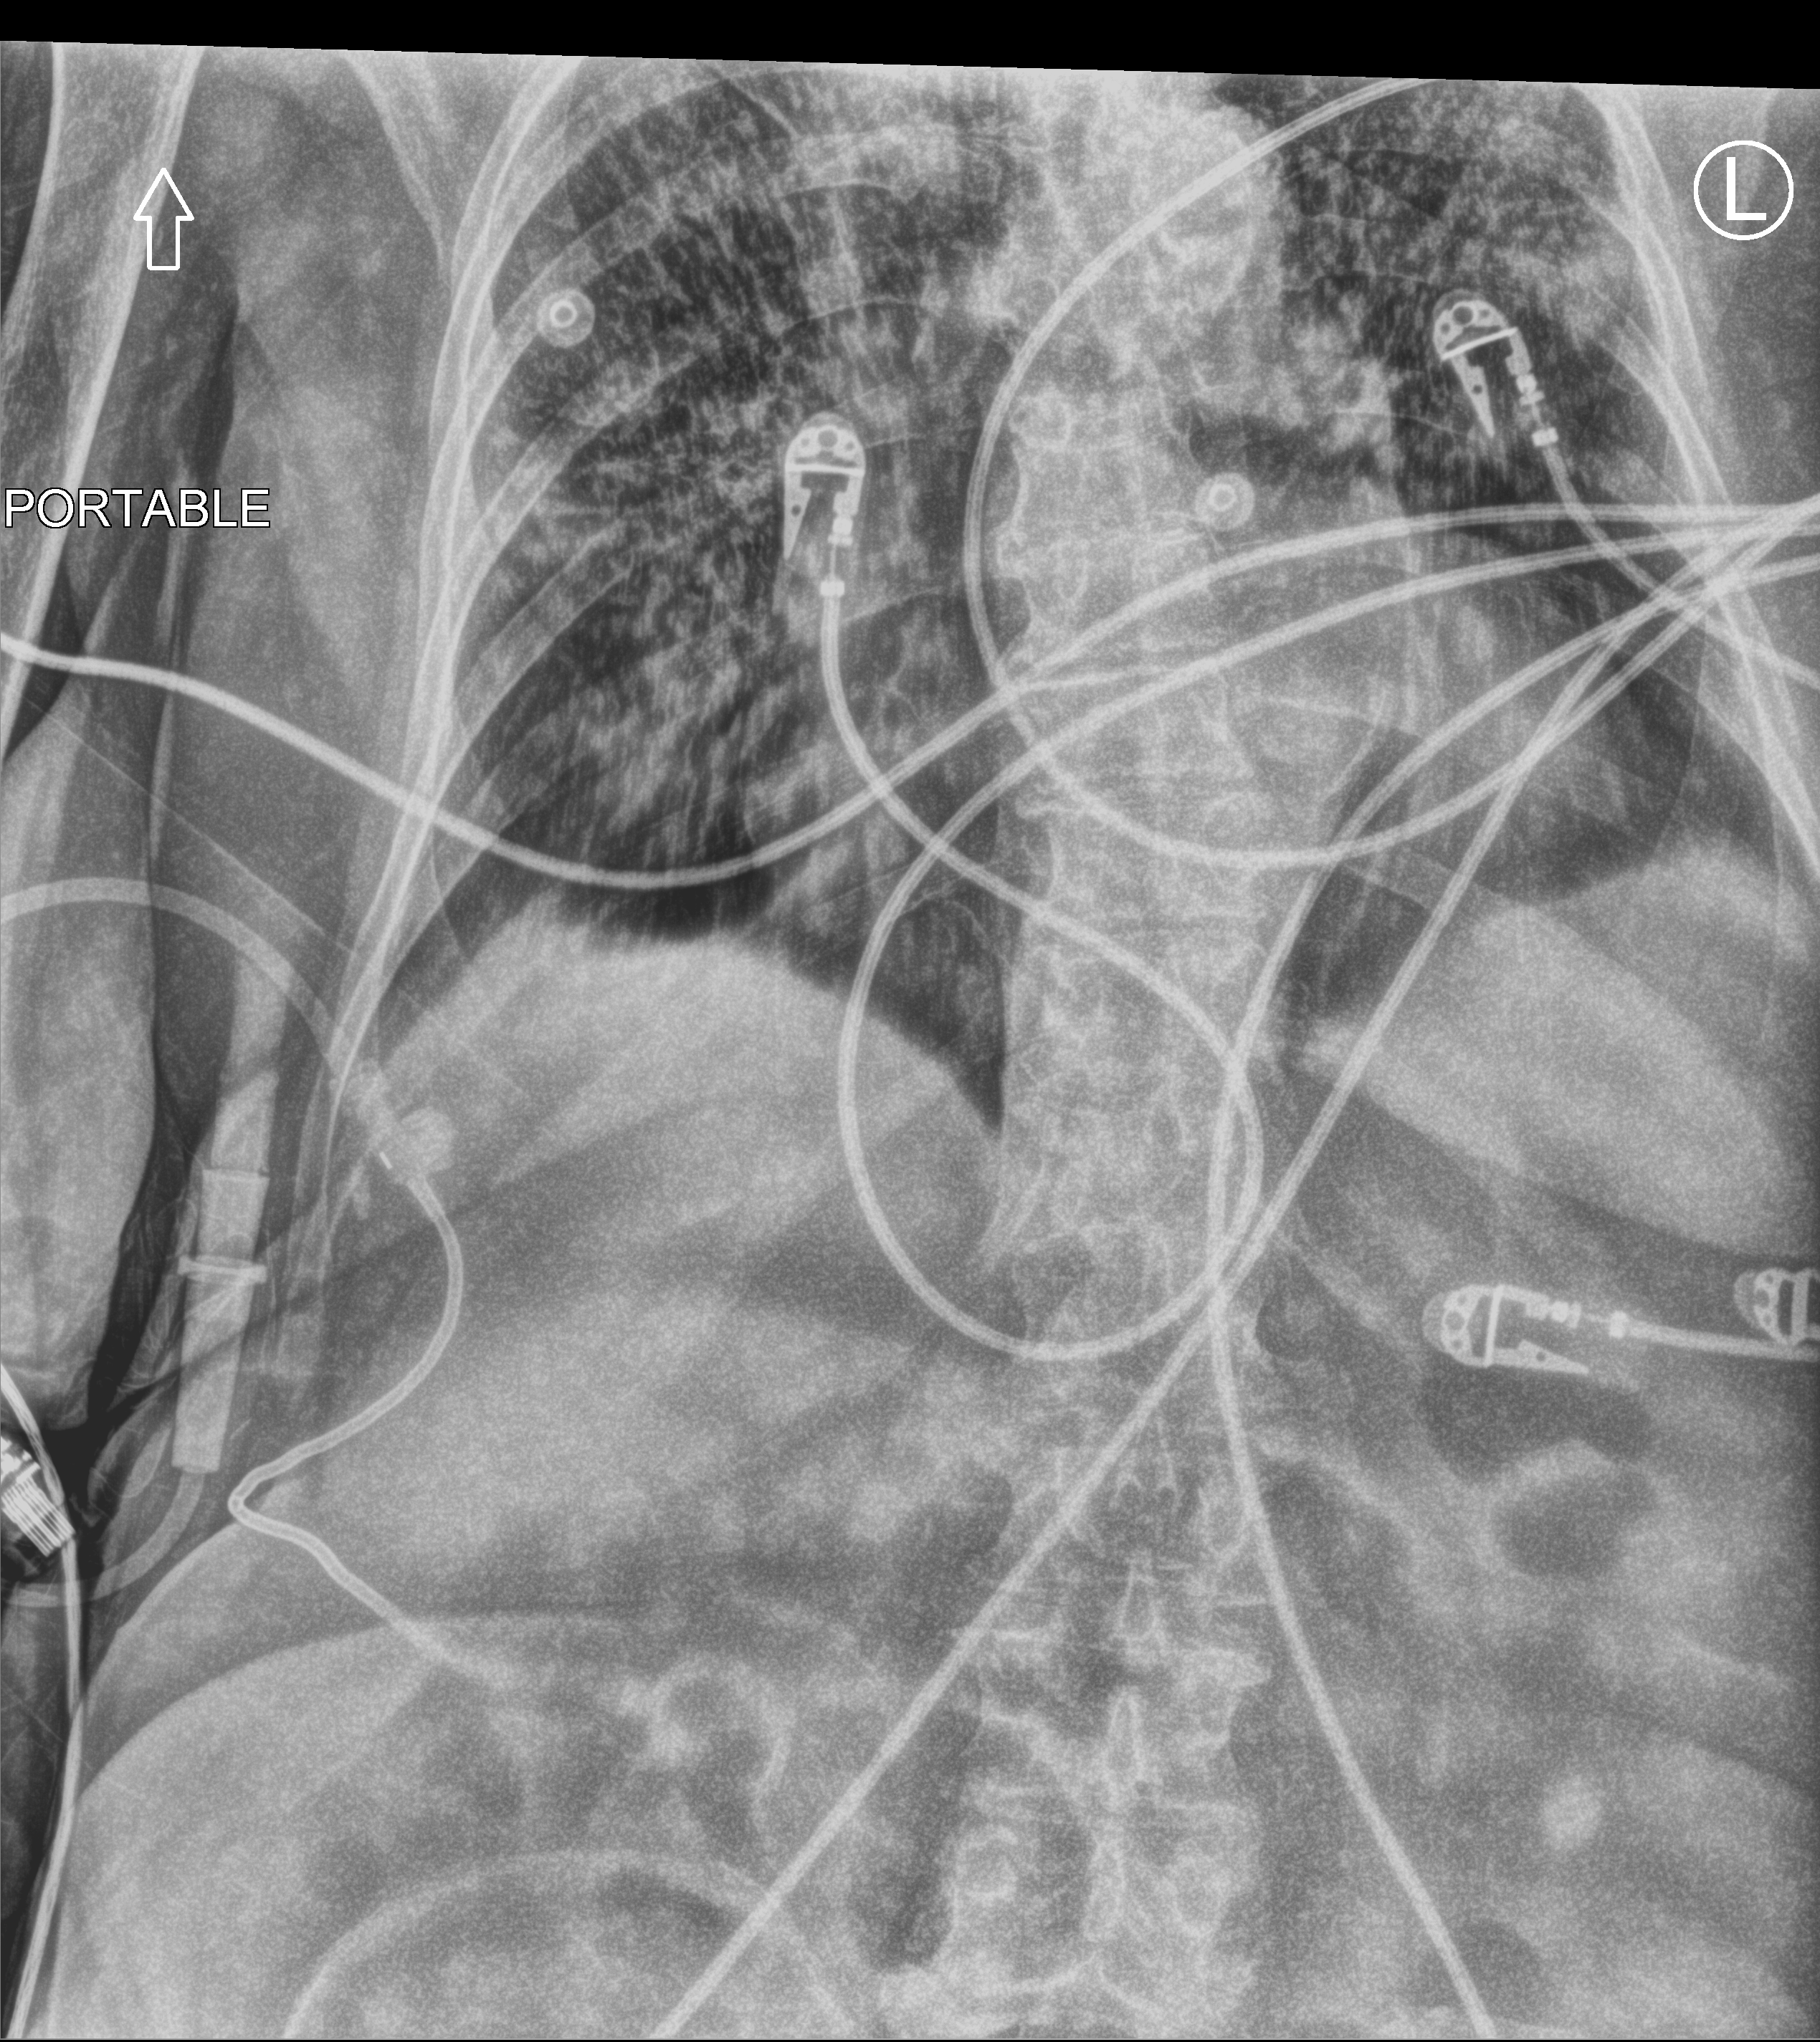
Bedside abdomen radiograph (computed radiography); anteroposterior (AP) projection. Female patient hospitalised with COVID-19, age 75–90 years.
Admission-level facts for this patient (not findings on this image; timing relative to this image not recorded):
- mechanically ventilated during this hospital stay: no